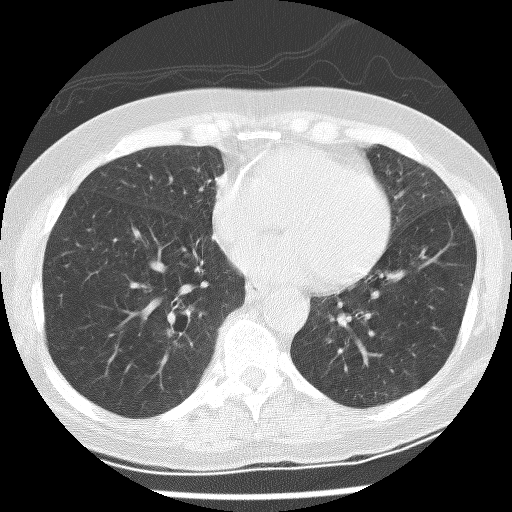
Chest CT (low-dose screening protocol), one axial image, baseline screening round, lung window (W 1500 / L -600 HU), 2.5 mm slice thickness, 512 × 512 image matrix. Female participant, aged 60 years at enrolment. Former smoker at enrolment.
- Expert-annotated lung lesion, bounding box (x1, y1, x2, y2) in pixels: (156, 321, 203, 358).
- Screening reader's record for this exam (one nodule recorded; not confirmed to be the boxed lesion): non-calcified nodule or mass ≥4 mm, right lower lobe, 10 × 6 mm, spiculated (stellate) margins, mixed attenuation.
- Lung cancer was diagnosed 275 days after this screen: adenocarcinoma with squamous metaplasia, right lower lobe, poorly differentiated (G3), stage IA (AJCC 6th edition), 23 mm at pathology.